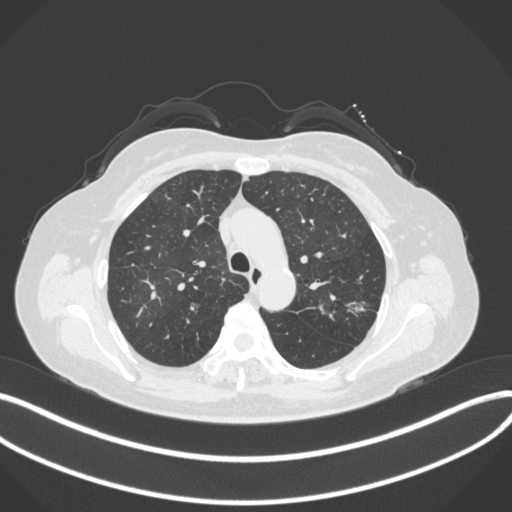
Chest CT, one axial slice; position 251 of 330 along the scan axis; lung window (W 1500 / L -600 HU); 1 mm slice thickness; 512 × 512 image matrix, field of view 400 × 400 mm. Patient: female, 60 years. From the clinical record (not read from this slice): clinical TNM (as recorded): T1c N0 M0.
Annotated regions visible in this slice (rectangle marked by the reading radiologist):
- lung tumour (recorded histology: adenocarcinoma): bounding box (x1, y1, x2, y2) in pixels: (341, 296, 365, 318)